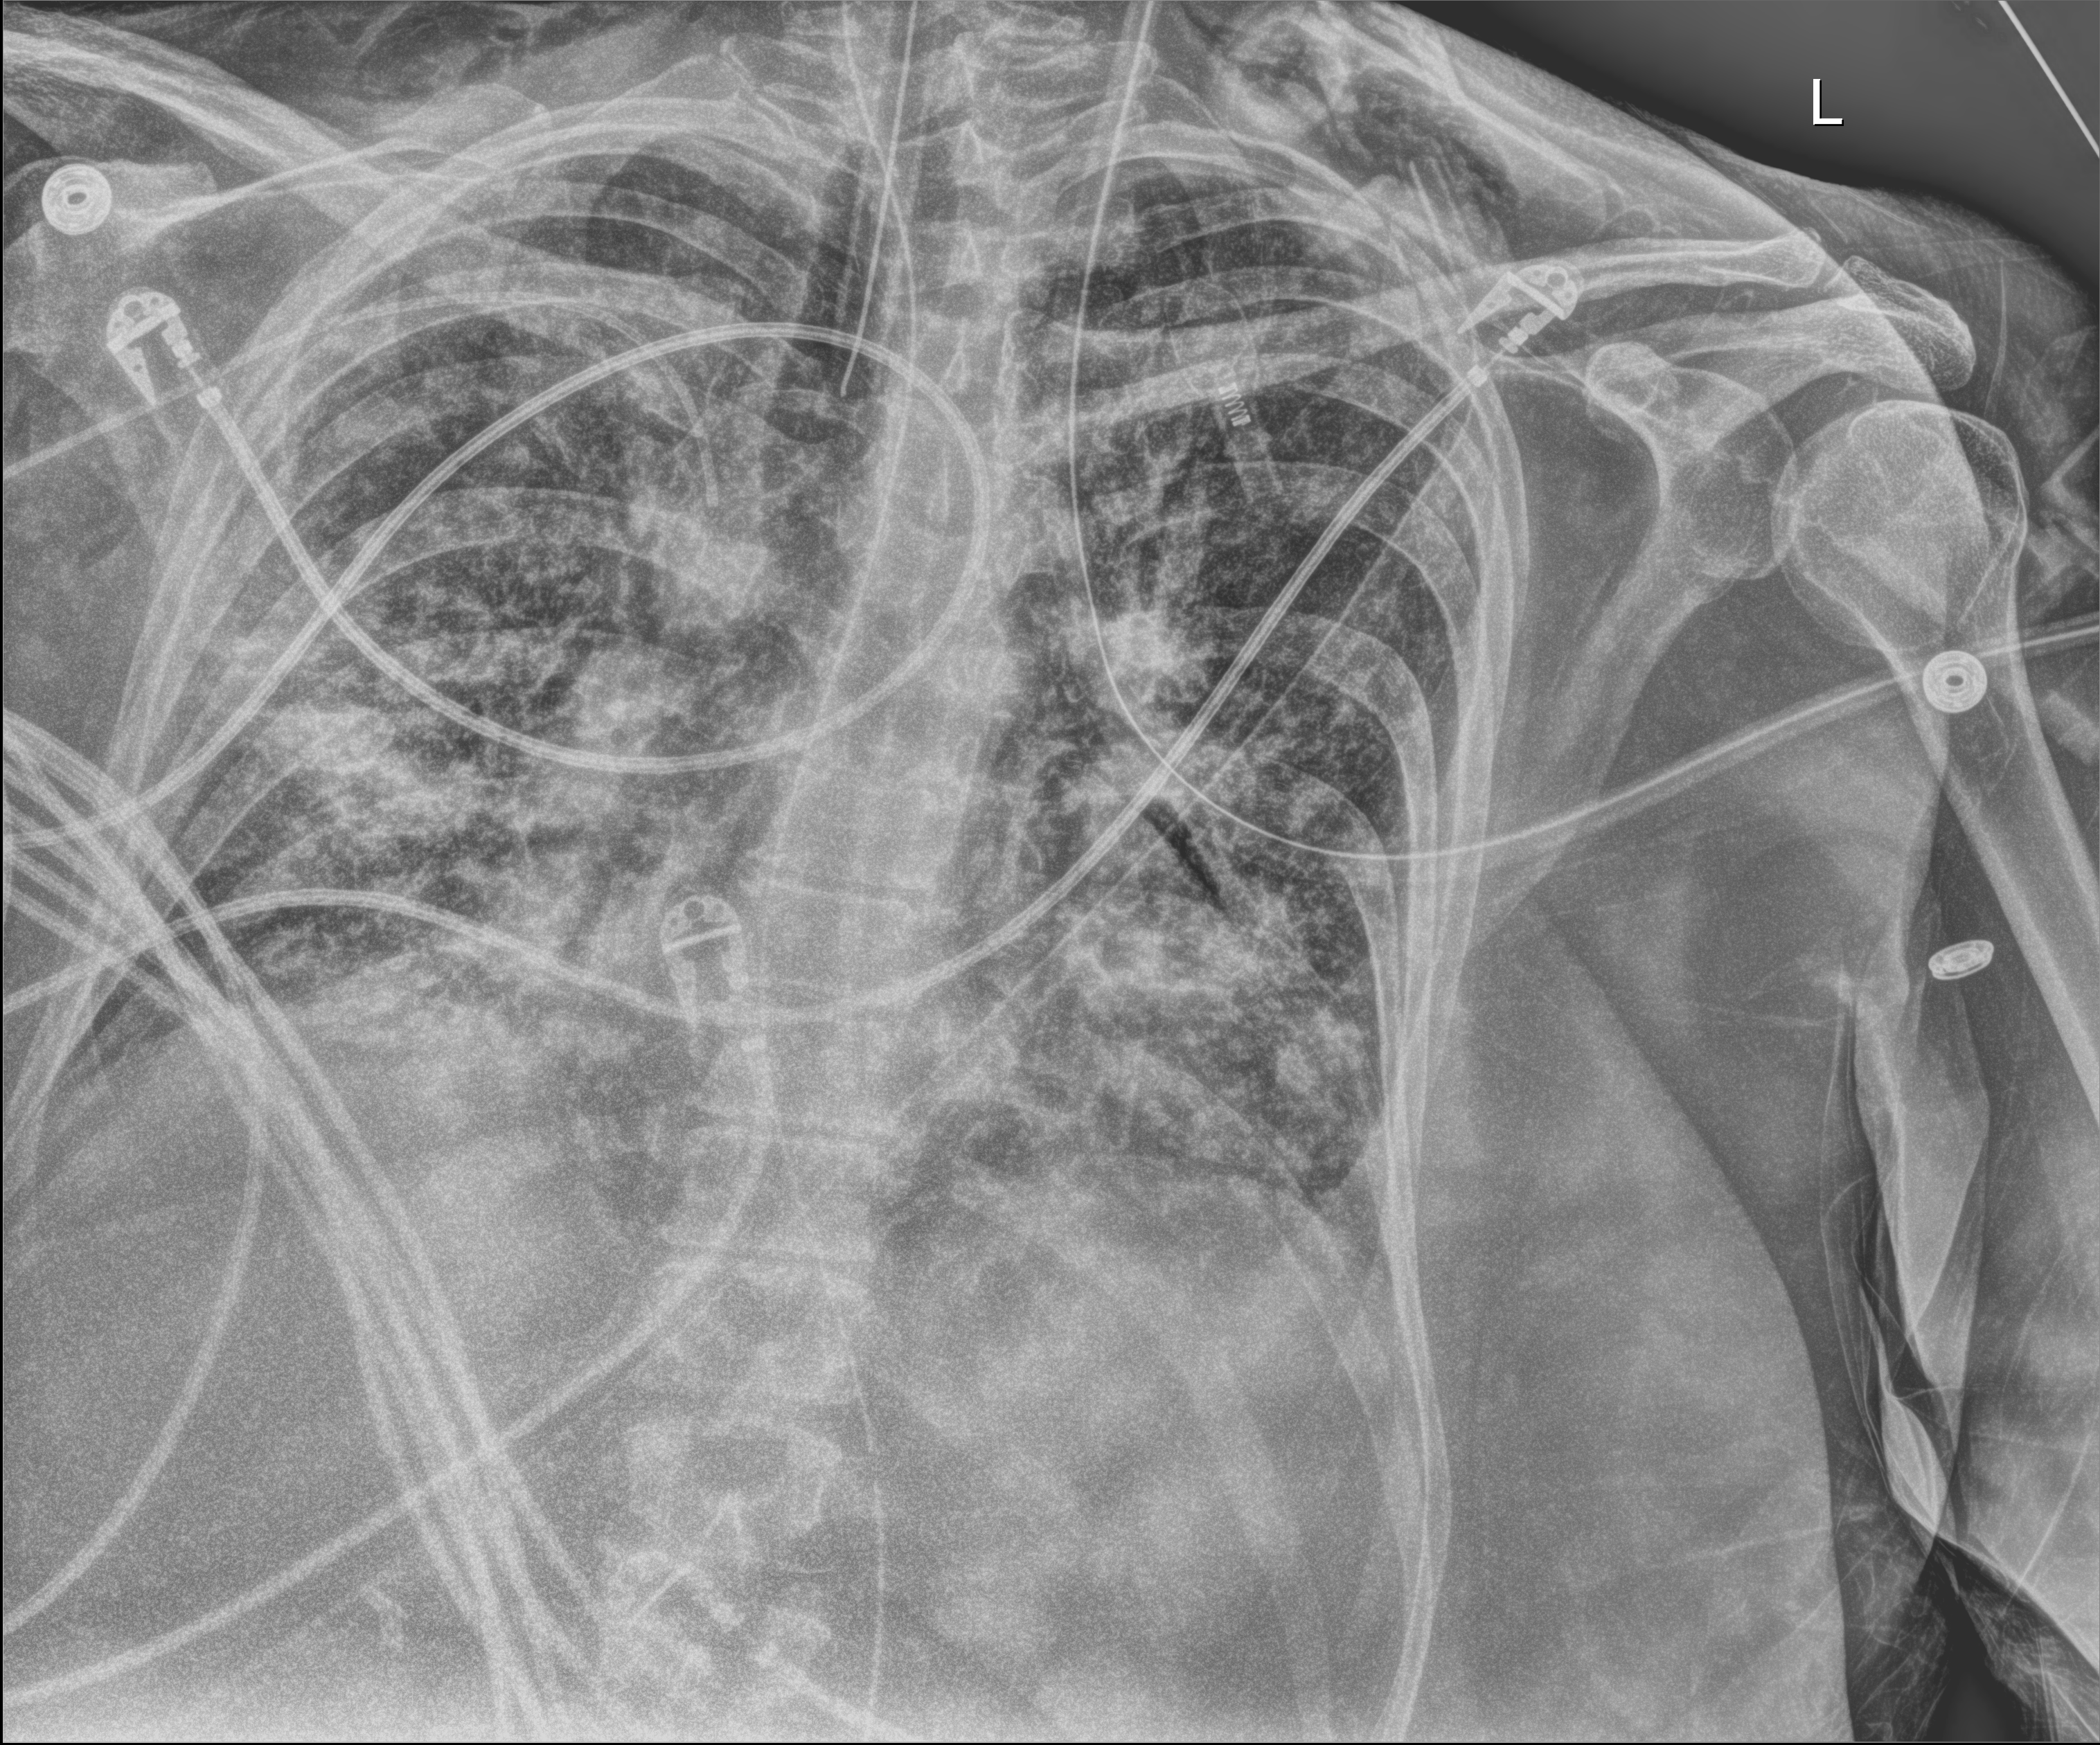
Portable chest radiograph; anteroposterior (AP) projection. Female patient hospitalised with COVID-19, age 60–74 years.
From the hospital-stay record, not from the radiograph (when in the stay this image was taken is not recorded): admitted to intensive care during this hospital stay: yes; chronic kidney disease (admission record): no.